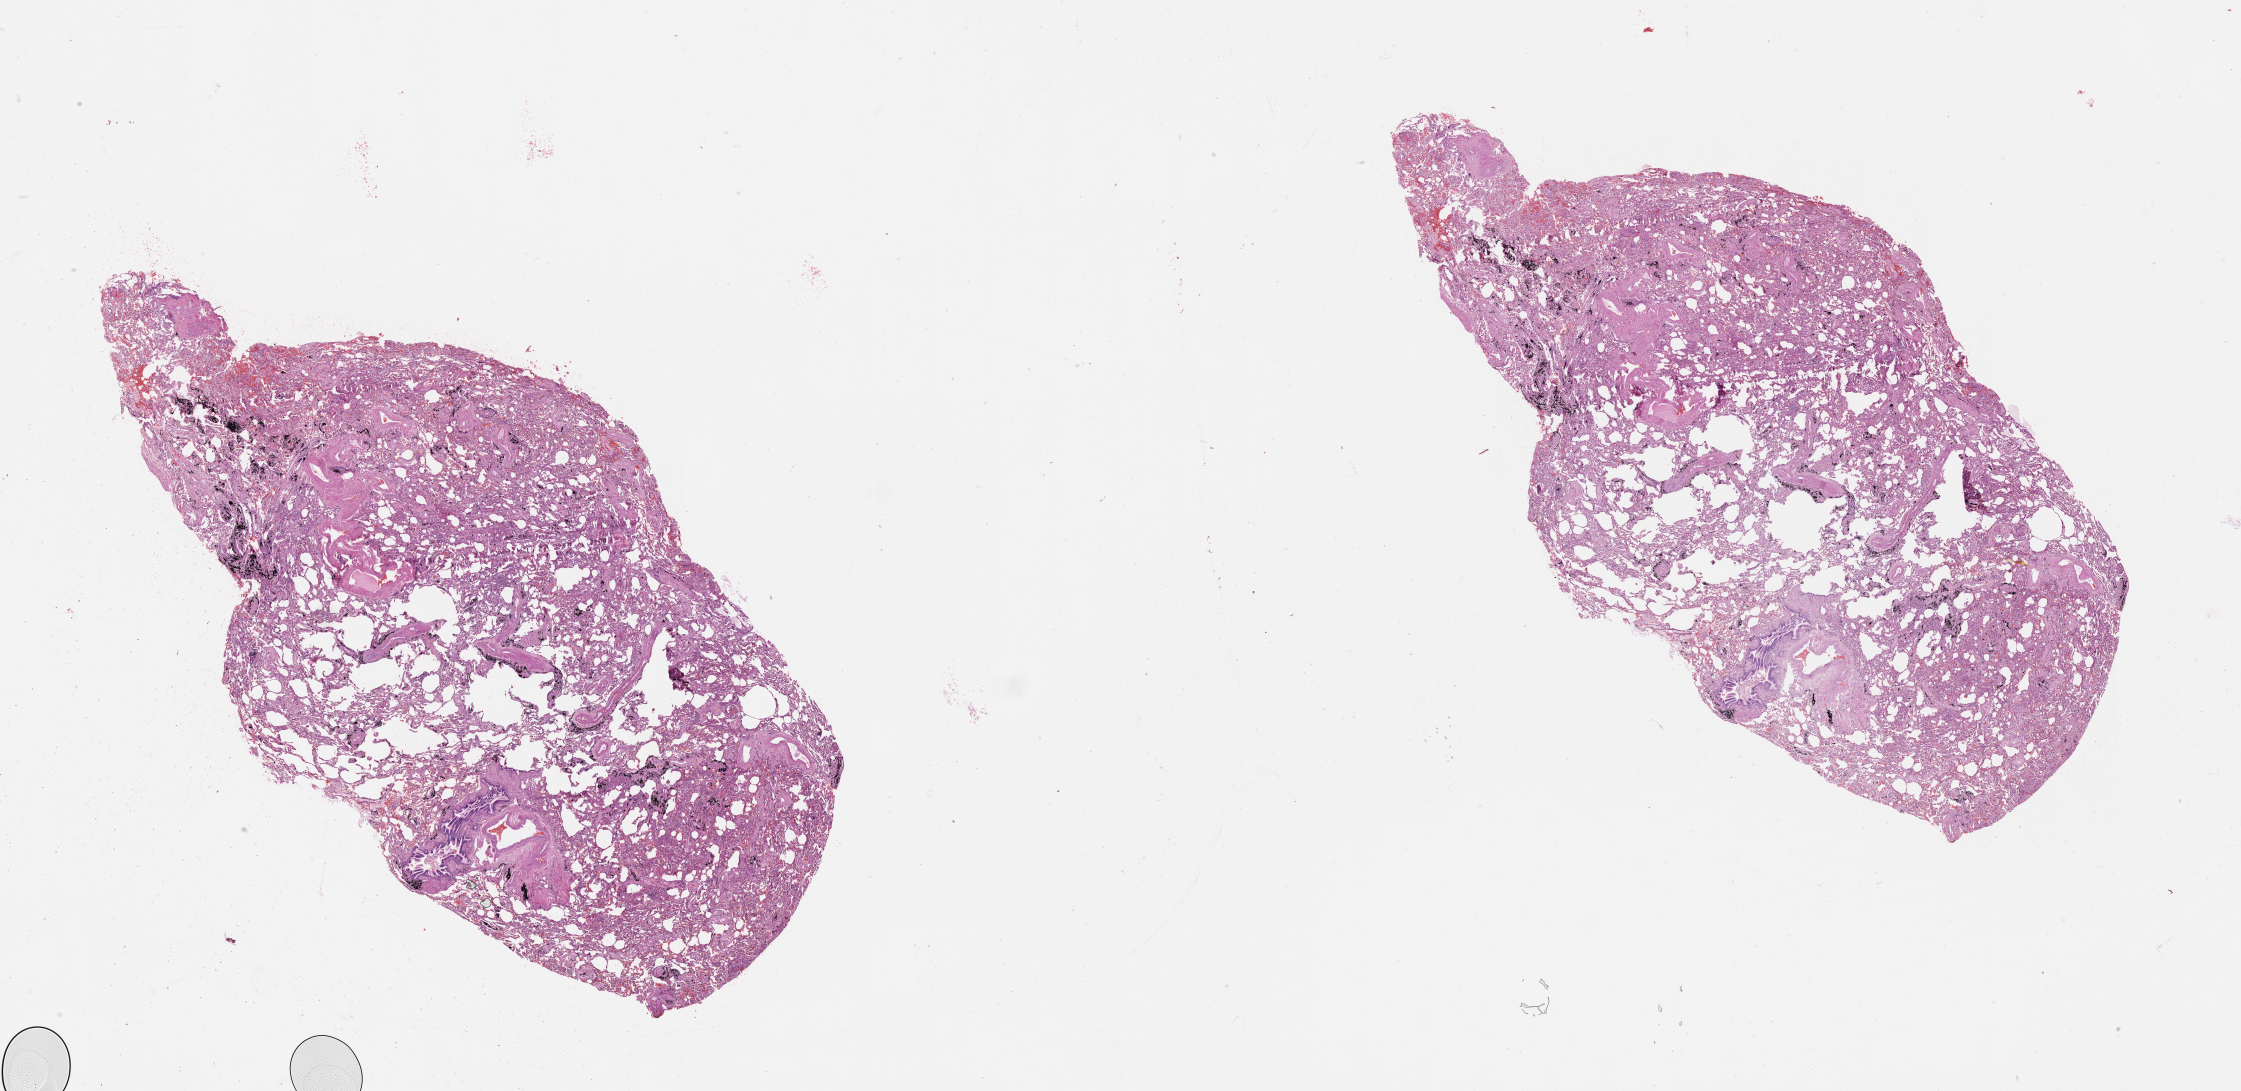
Digitized Hematoxylin and eosin (H&E) stained tissue section (whole slide), whole scanned area (about 36.1 x 17.6 mm) shown as a low-resolution overview; lung, tissue type not recorded.
* patient diagnosis (cohort enrolment): squamous cell carcinoma (lung)